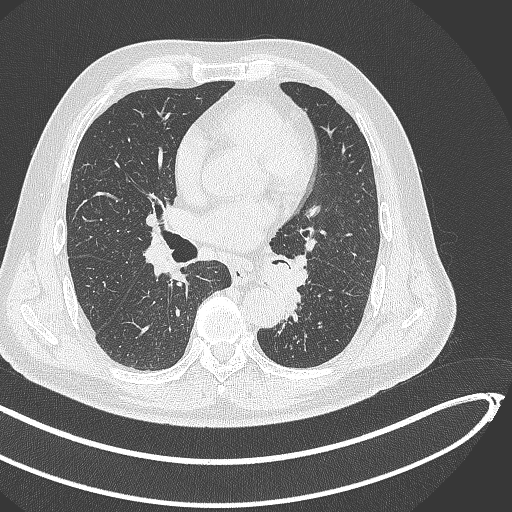
Chest CT, one axial slice. Position 245 of 468 along the scan axis. Lung window (W 1500 / L -600 HU). 512 × 512 image matrix, field of view 400 × 400 mm. Patient: male, 64 years. Case-level facts recorded for this patient, not image findings: clinical TNM (as recorded): T1c N0 M0; histopathological grade: G2.
Structures marked on this image (bounding box drawn by a radiologist):
- lung tumour (recorded histology: squamous cell carcinoma): box from (x=258, y=258) to (x=305, y=318) px